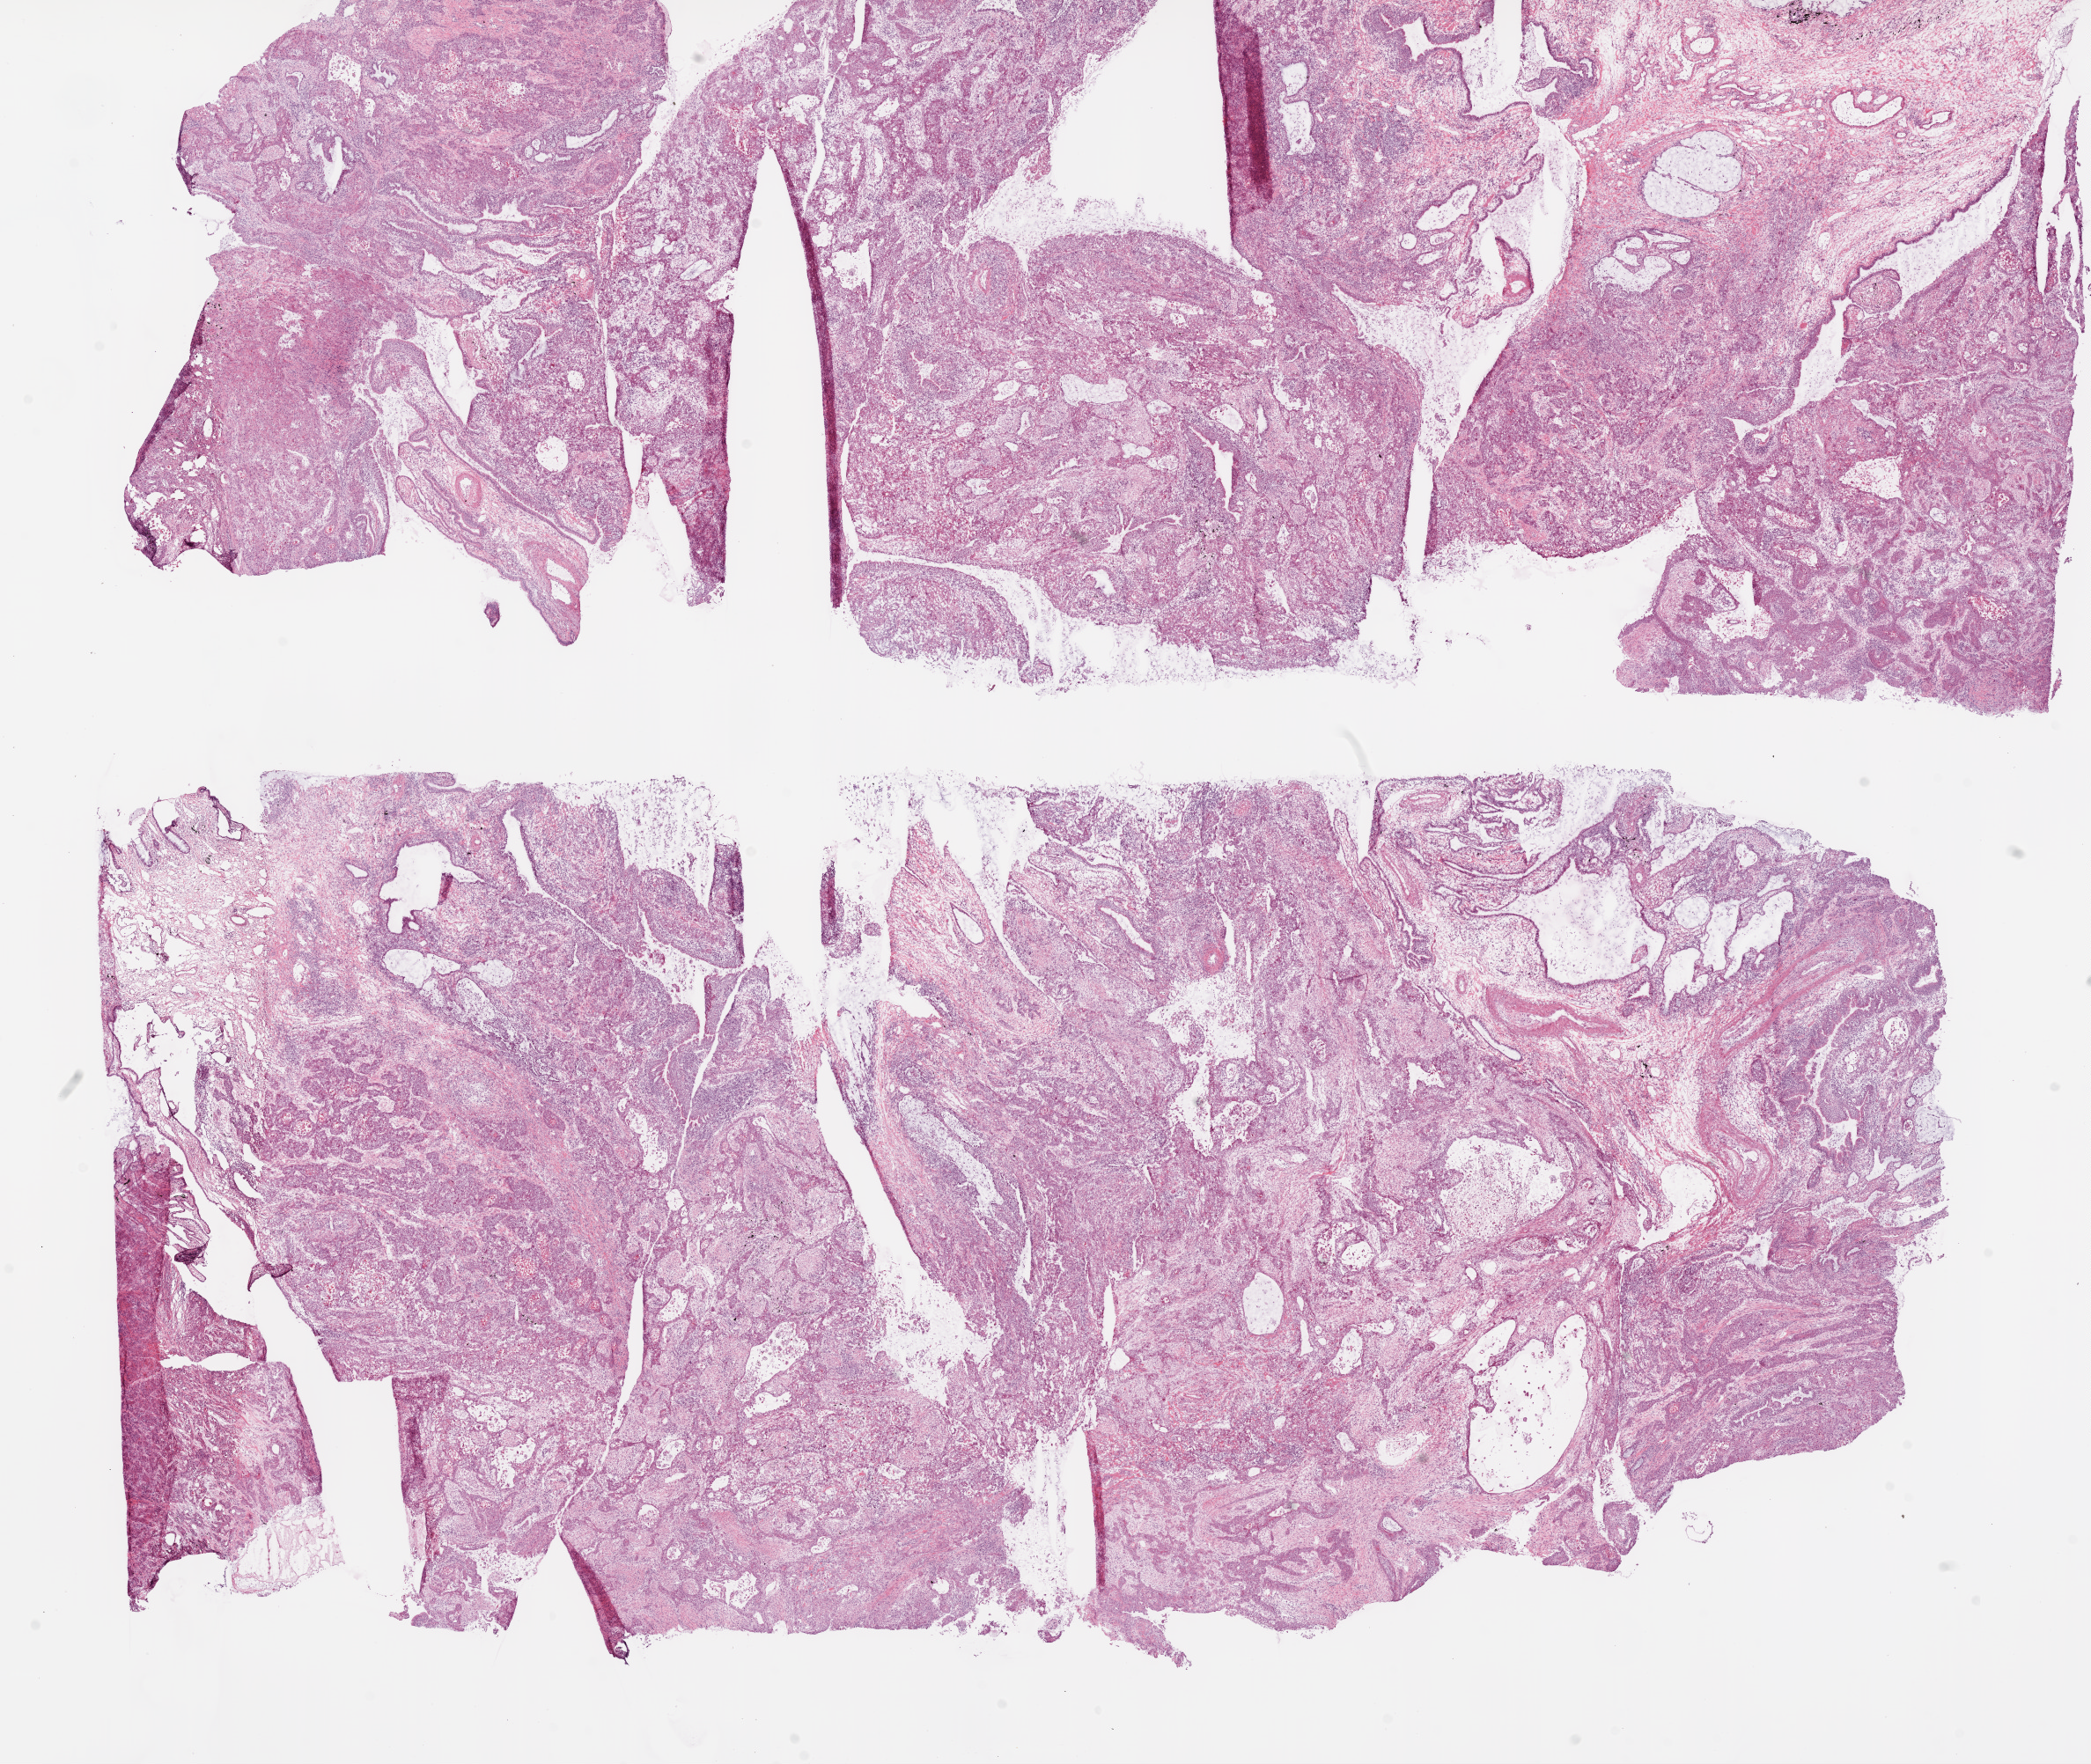
Hematoxylin and eosin (H&E) stained whole-slide image — a low-resolution overview of the entire scanned area, about 19.1 x 16.1 mm (from a 20x scan), frozen section, sample: primary tumour, lung. Patient: male, age at initial diagnosis 75 years. Slide review estimates, as recorded: tumour cells 62%, tumour nuclei 70%, normal cells 3%, stromal cells 30%, necrosis 5%.
Laterality: right. Diagnosis: Squamous cell carcinoma, NOS (upper lobe, lung). AJCC pathologic stage: IIIA.